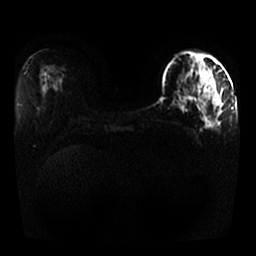
Breast MRI, one axial slice; position 13 of 25 along the scan axis; diffusion-weighted series; image 2 of 4 stored at this slice position (different b-values; order by instance number); 1.5 T; 256 × 256 image matrix, field of view 330 × 330 mm. Female patient.
Structures marked on this image (expert manual segmentation):
- tumour on diffusion-weighted imaging: bounding box [x1, y1, x2, y2] px = [213, 97, 219, 104]